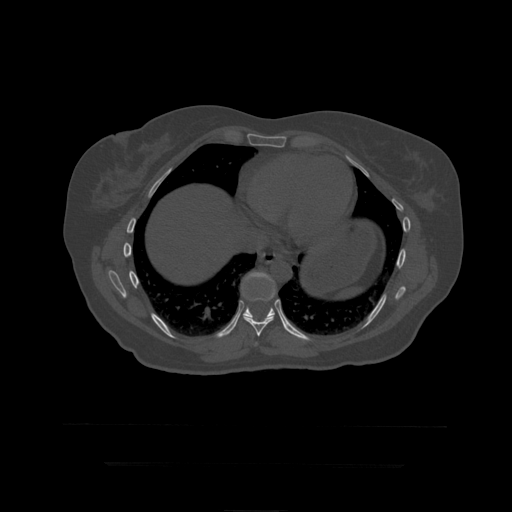
CT including the spine, one axial slice; position 254 of 399 along the scan axis; reconstruction kernel STANDARD; 120 kVp; bone window (W 1800 / L 400 HU); 1.25 mm slice thickness; 512 × 512 image matrix, field of view 450 × 450 mm. Patient age 41 years. Case-level facts recorded for this patient, not image findings: primary cancer: breast.
Annotated regions visible in this slice (semi-automatic segmentation, software-assisted and operator-edited):
- T10 vertebra: bounding box [x1, y1, x2, y2] px = [242, 272, 290, 333]
- T8 vertebra: [256, 342, 258, 345]
- T9 vertebra: [243, 285, 280, 337]